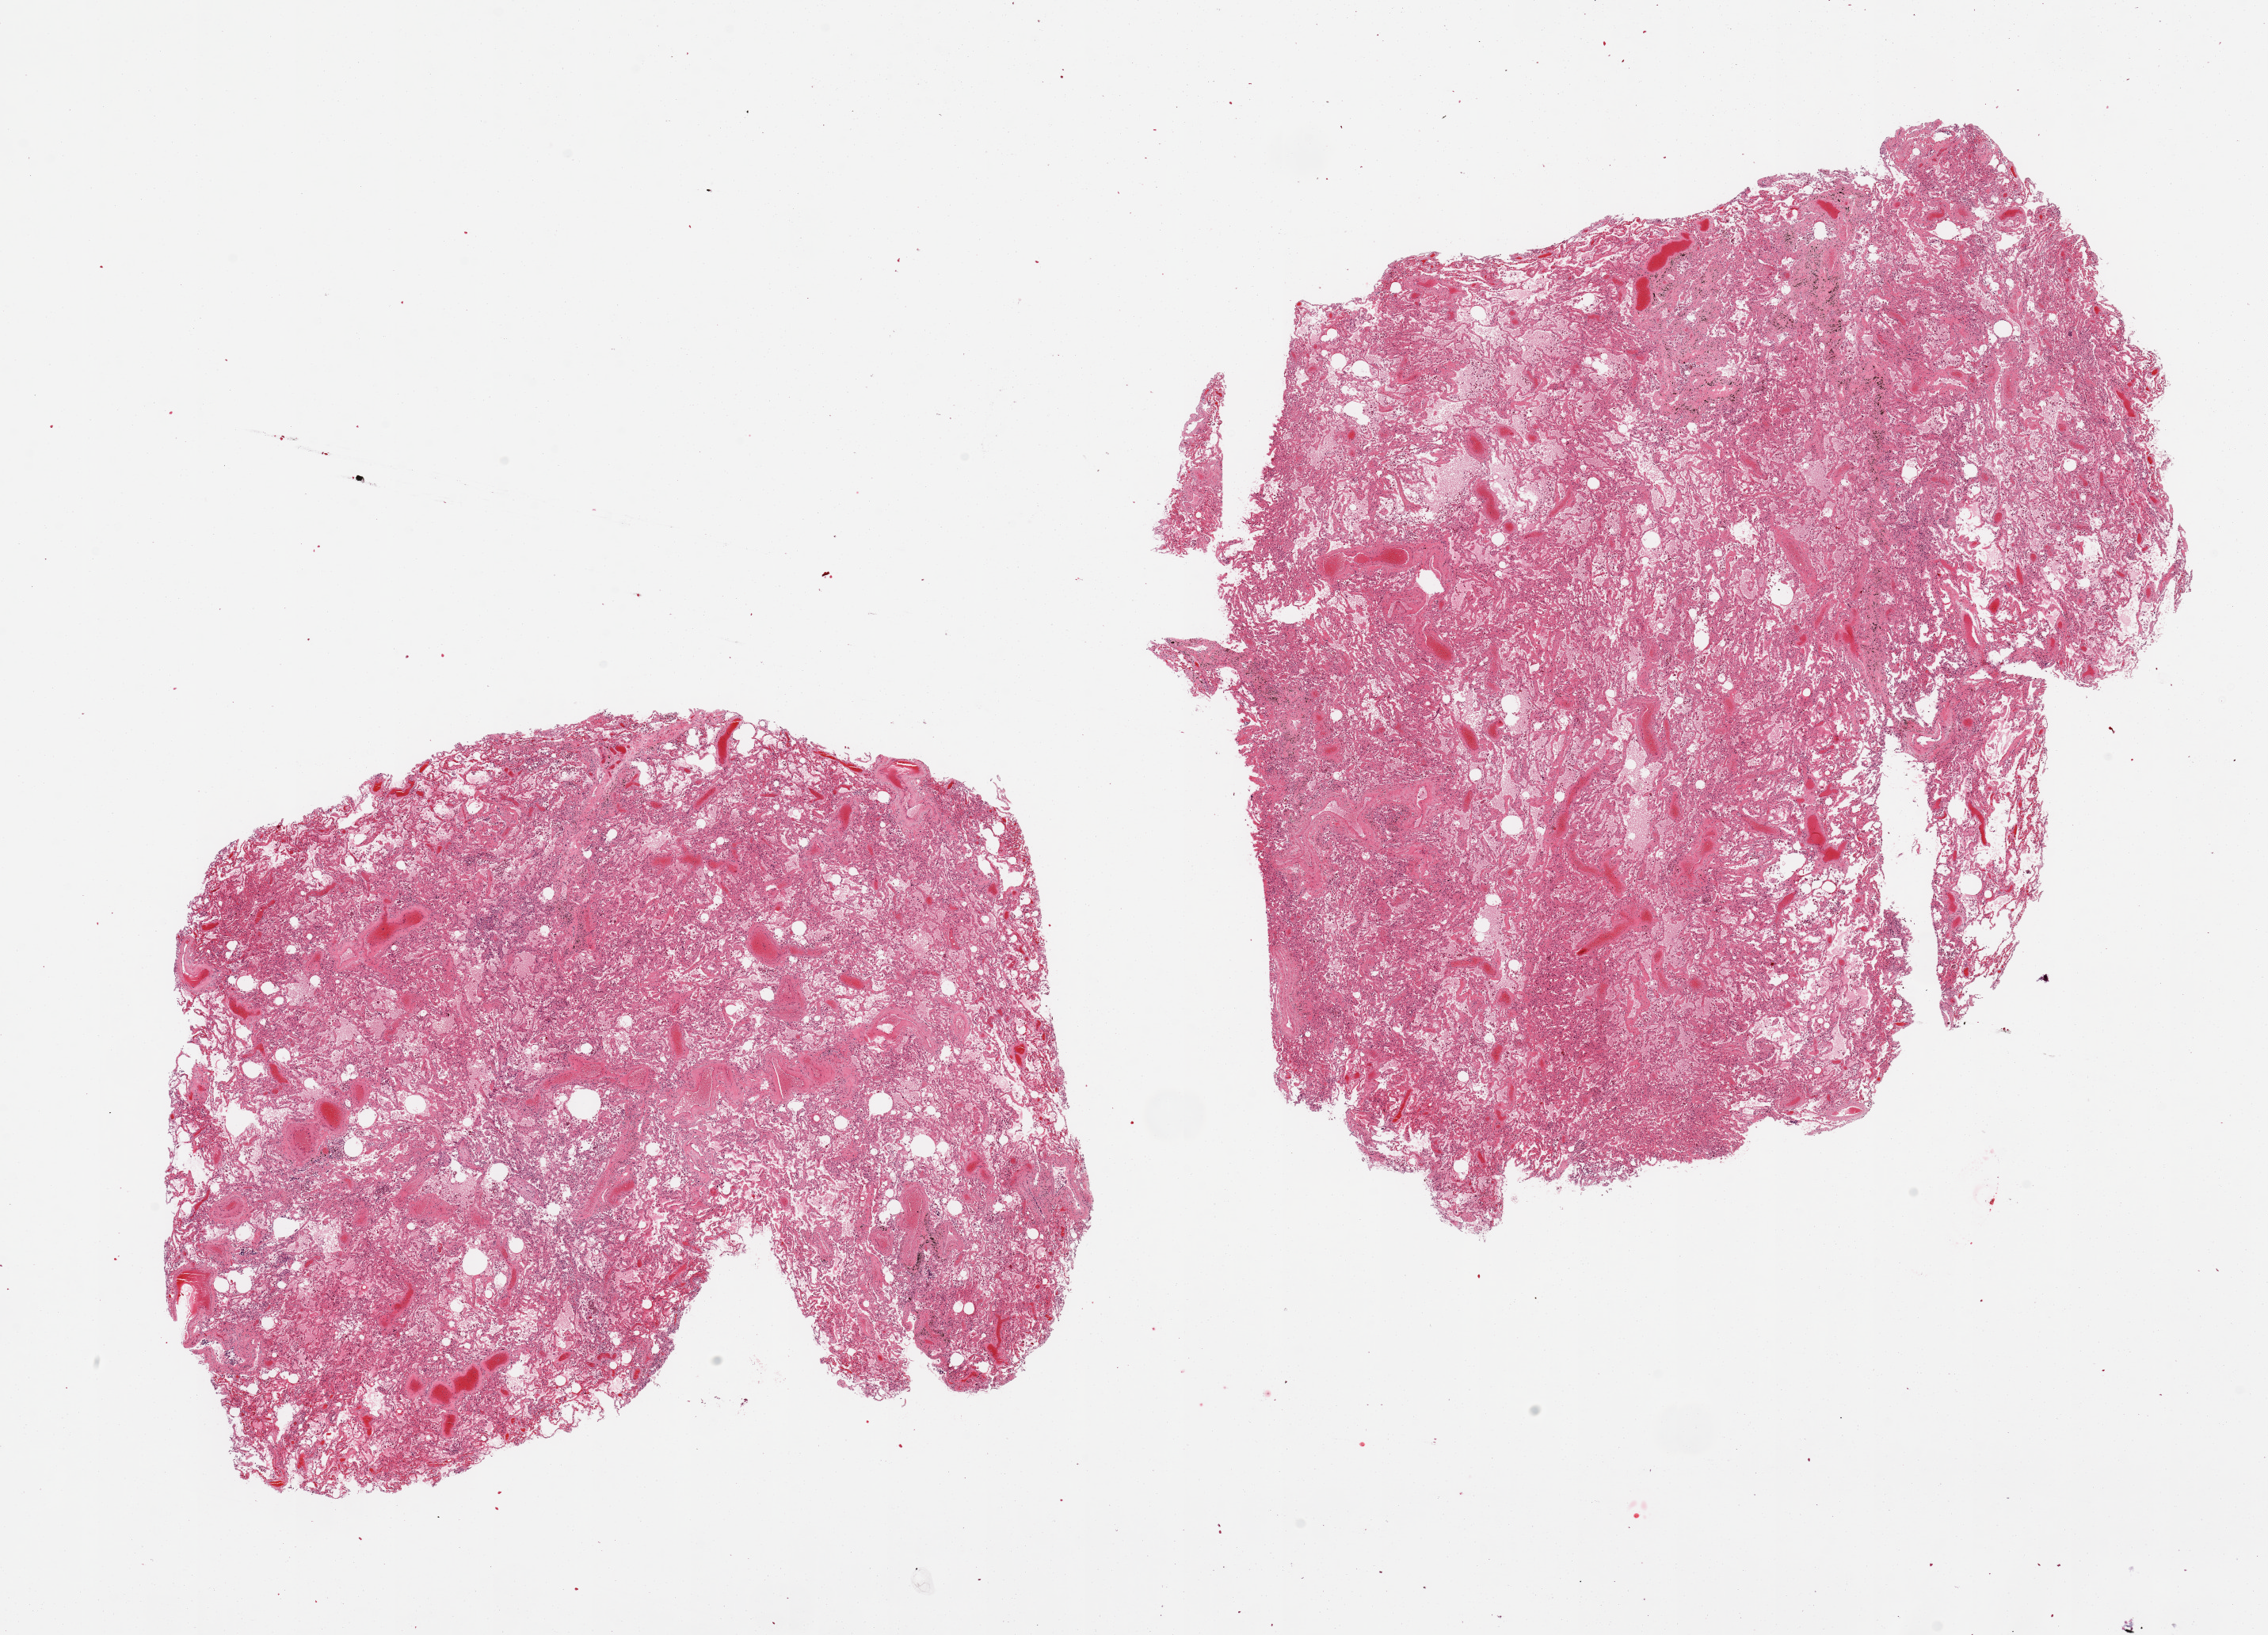
Whole-slide image, H&E stain — shown as a low-resolution overview of the whole scanned area (about 22.6 x 16.3 mm). PAXgene-fixed, paraffin-embedded tissue. Sampled site (target tissue): lung. Donor tissue sample.
Review note (as recorded): 2 pieces, moderate-marked congestion/edema, bronchial mucosa sloughed.